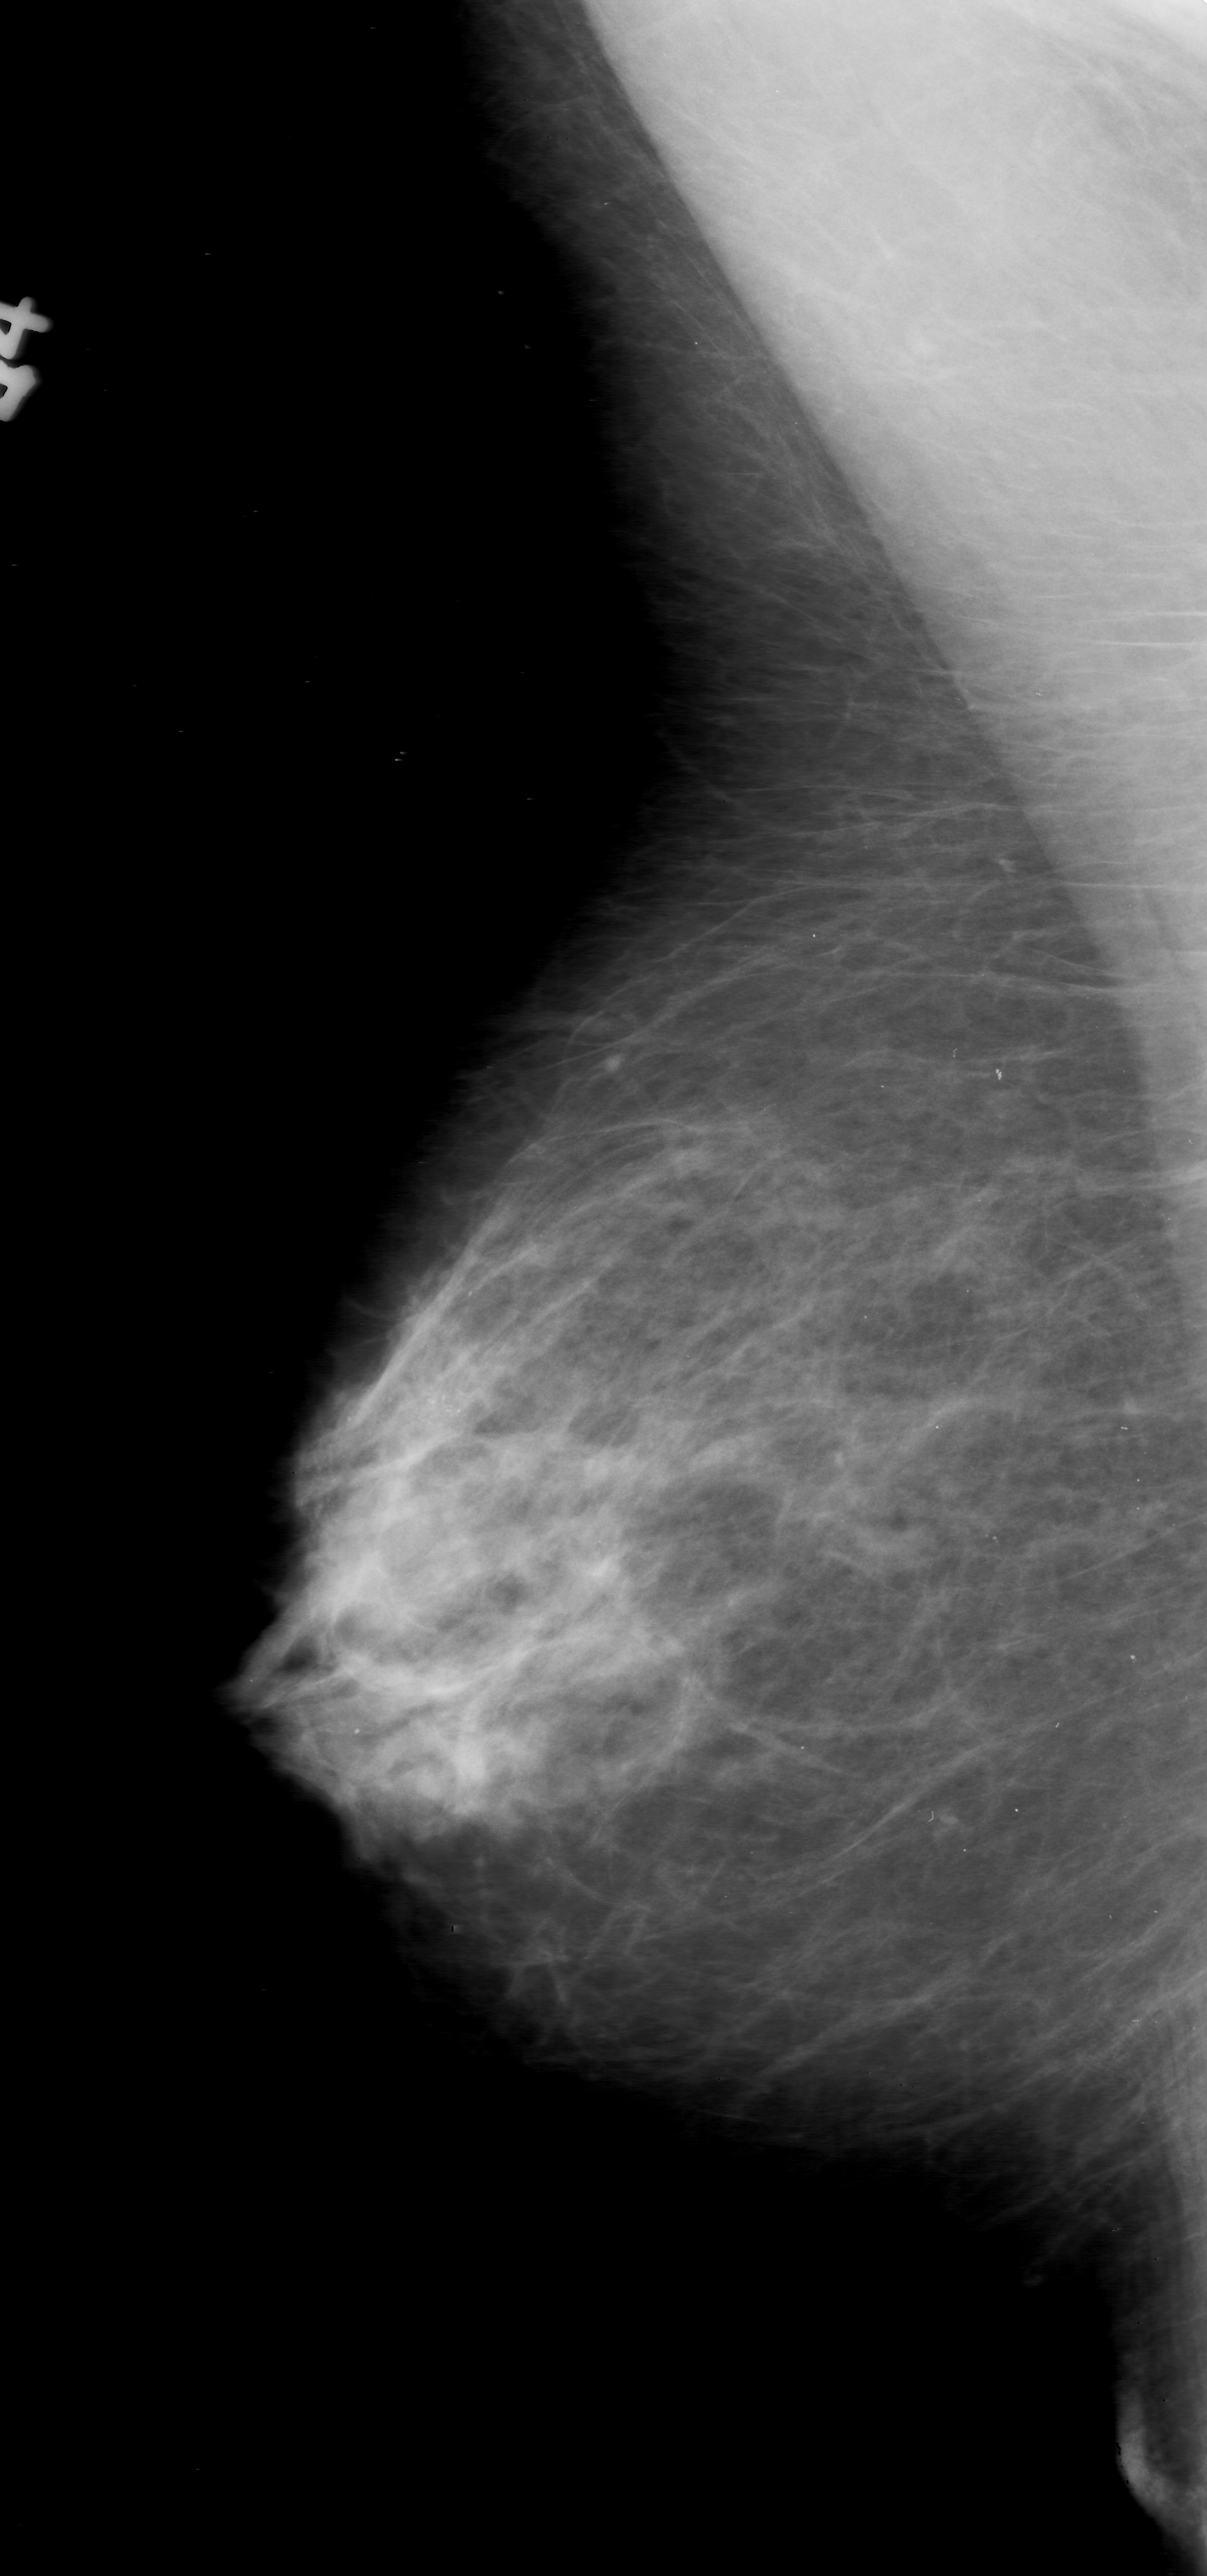
Scanned film-screen mammogram. Right breast. MLO view. BI-RADS breast density category 2 (scale 1–4). 1207 × 2576 image matrix.
Expert-marked regions of interest on this image (one box per marked abnormality):
- calcifications, morphology pleomorphic, distribution clustered; BI-RADS assessment category 0 (incomplete: needs additional imaging); pathology (as recorded): malignant: bounding box <277,1286,565,1522> (left, top, right, bottom; pixels)